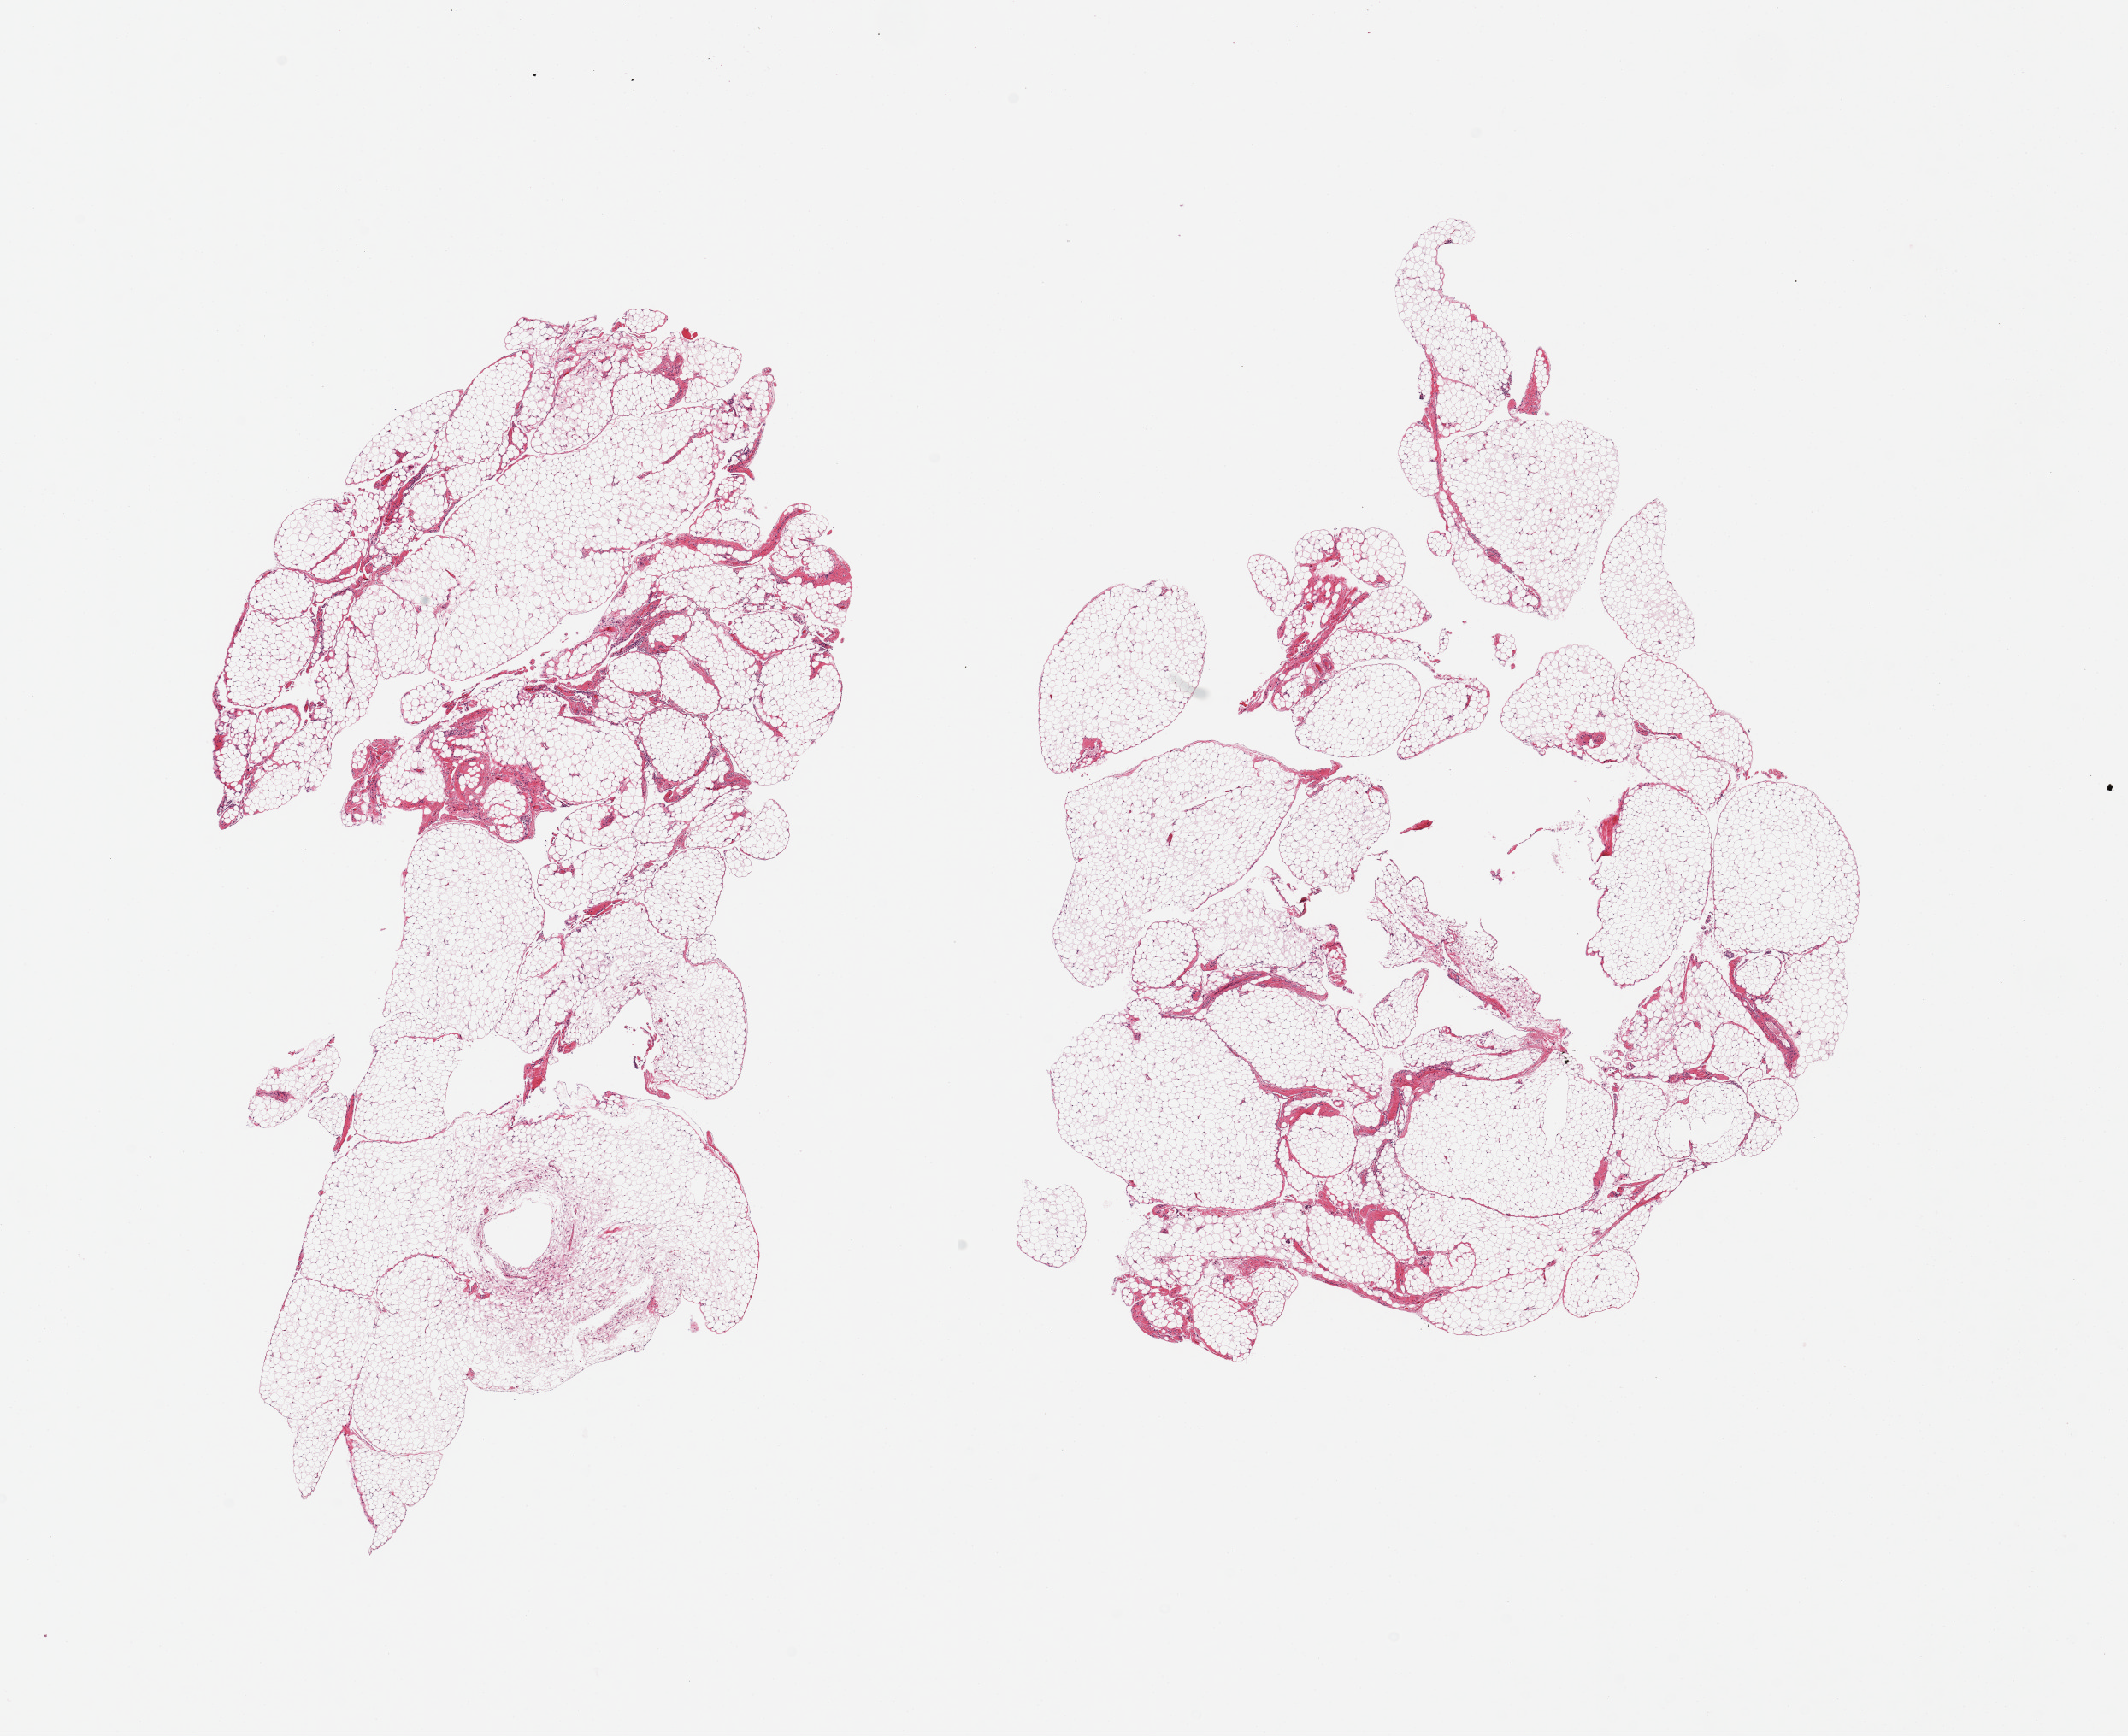
Whole-slide image, H&E stain, brightfield, whole scanned area (about 19.7 x 16.1 mm) shown as a low-resolution overview; PAXgene-fixed, paraffin-embedded tissue; target tissue: omentum; donor tissue sample. Male donor.
Review note (as recorded): 2 pieces, no abnormalities; fascia/vascular elements are ~5-10% of tissue.